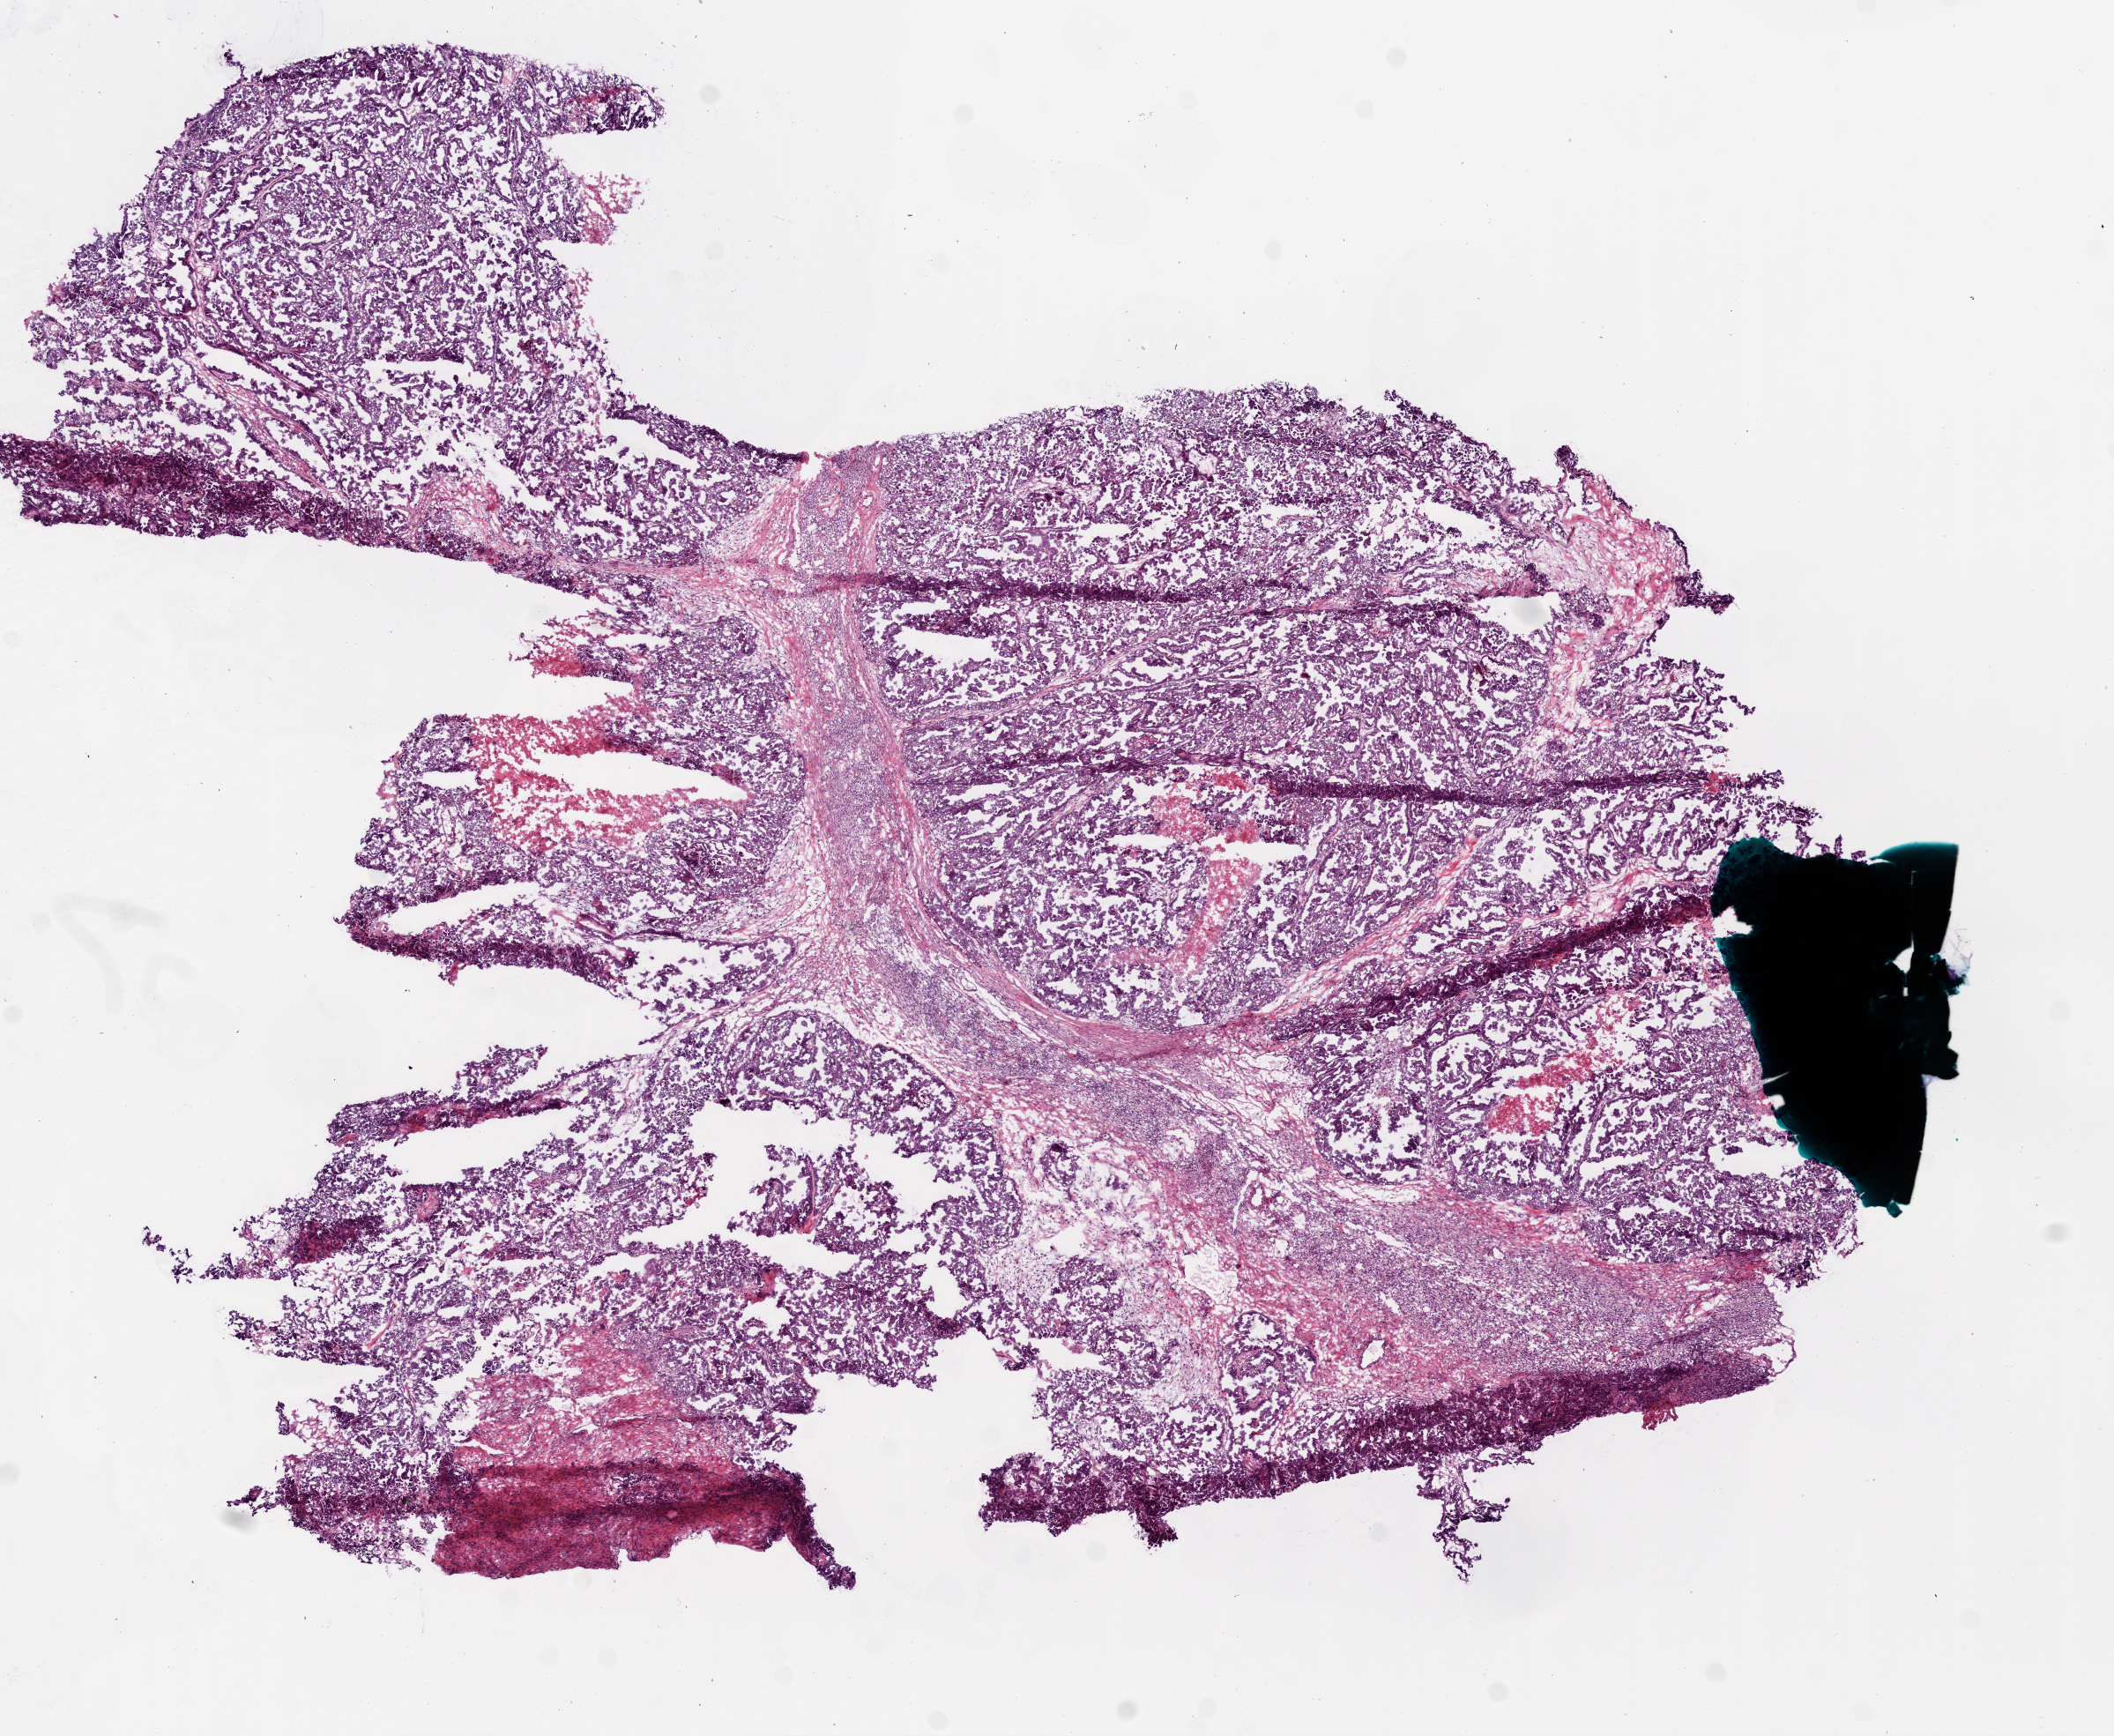
Whole-slide histology image, Hematoxylin and eosin (H&E) stained, shown as a low-resolution overview of the whole scanned area (about 9.7 x 7.9 mm, slide scanned at 20x), frozen section, ovary, primary tumour sample. Female, age 63 years at initial diagnosis. Histologic grade: G3 (poorly differentiated). Pathologist review of this section (percent, as recorded): tumour nuclei 95%, necrosis 5%.
- laterality: right
- FIGO stage: IIIC
- histologic diagnosis: Serous cystadenocarcinoma, NOS